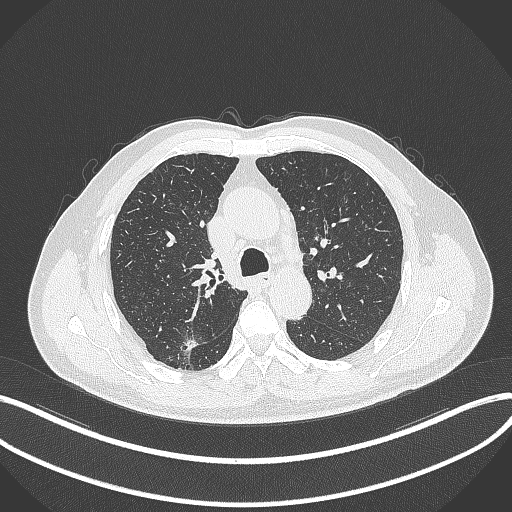
Chest CT, one axial slice; position 252 of 359 along the scan axis; 120 kVp; lung window (W 1500 / L -600 HU); 1 mm slice thickness; 512 × 512 image matrix, field of view 400 × 400 mm. Male patient, age 69 years. From the clinical record (not read from this slice): clinical TNM (as recorded): T1b N0 M0; histopathological grade: G2-3.
Structures marked on this image (bounding box drawn by a radiologist):
- lung tumour (recorded histology: adenocarcinoma): bounding box <184,336,201,352> (left, top, right, bottom; pixels)